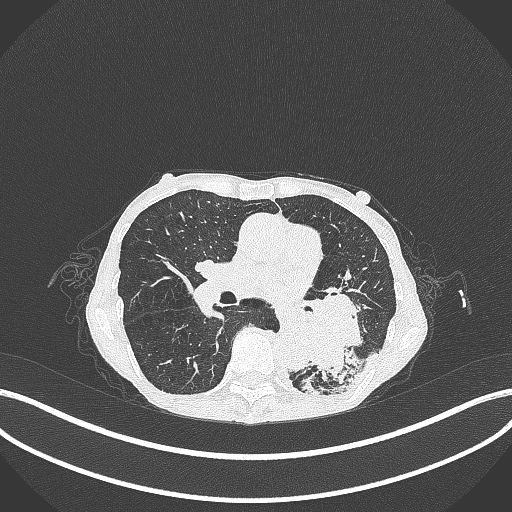
Chest CT, one axial slice. Position 141 of 347 along the scan axis. Lung window (W 1500 / L -600 HU). 1 mm slice thickness. 512 × 512 image matrix, field of view 400 × 400 mm. Female patient, age 70 years. From the clinical record (not read from this slice): clinical TNM (as recorded): T3 N0 M0.
Structures marked on this image (rectangle marked by the reading radiologist):
- lung tumour (recorded histology: small cell carcinoma): bounding box (x1, y1, x2, y2) in pixels: (294, 286, 369, 388)